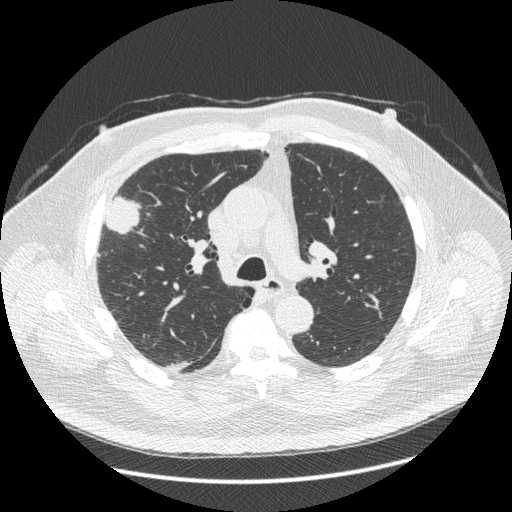
Low-dose screening chest CT, one axial slice. Position 281 of 426 along the scan axis. Reconstruction kernel STANDARD. 120 kVp. Lung window (W 1500 / L -600 HU). 1.25 mm slice thickness. 512 × 512 image matrix, field of view 400 × 400 mm.
Outlined on this slice (expert manual segmentation):
- lesion 1 (tumor, upper lobe of right lung): bounding box [x1, y1, x2, y2] px = [106, 197, 139, 234]